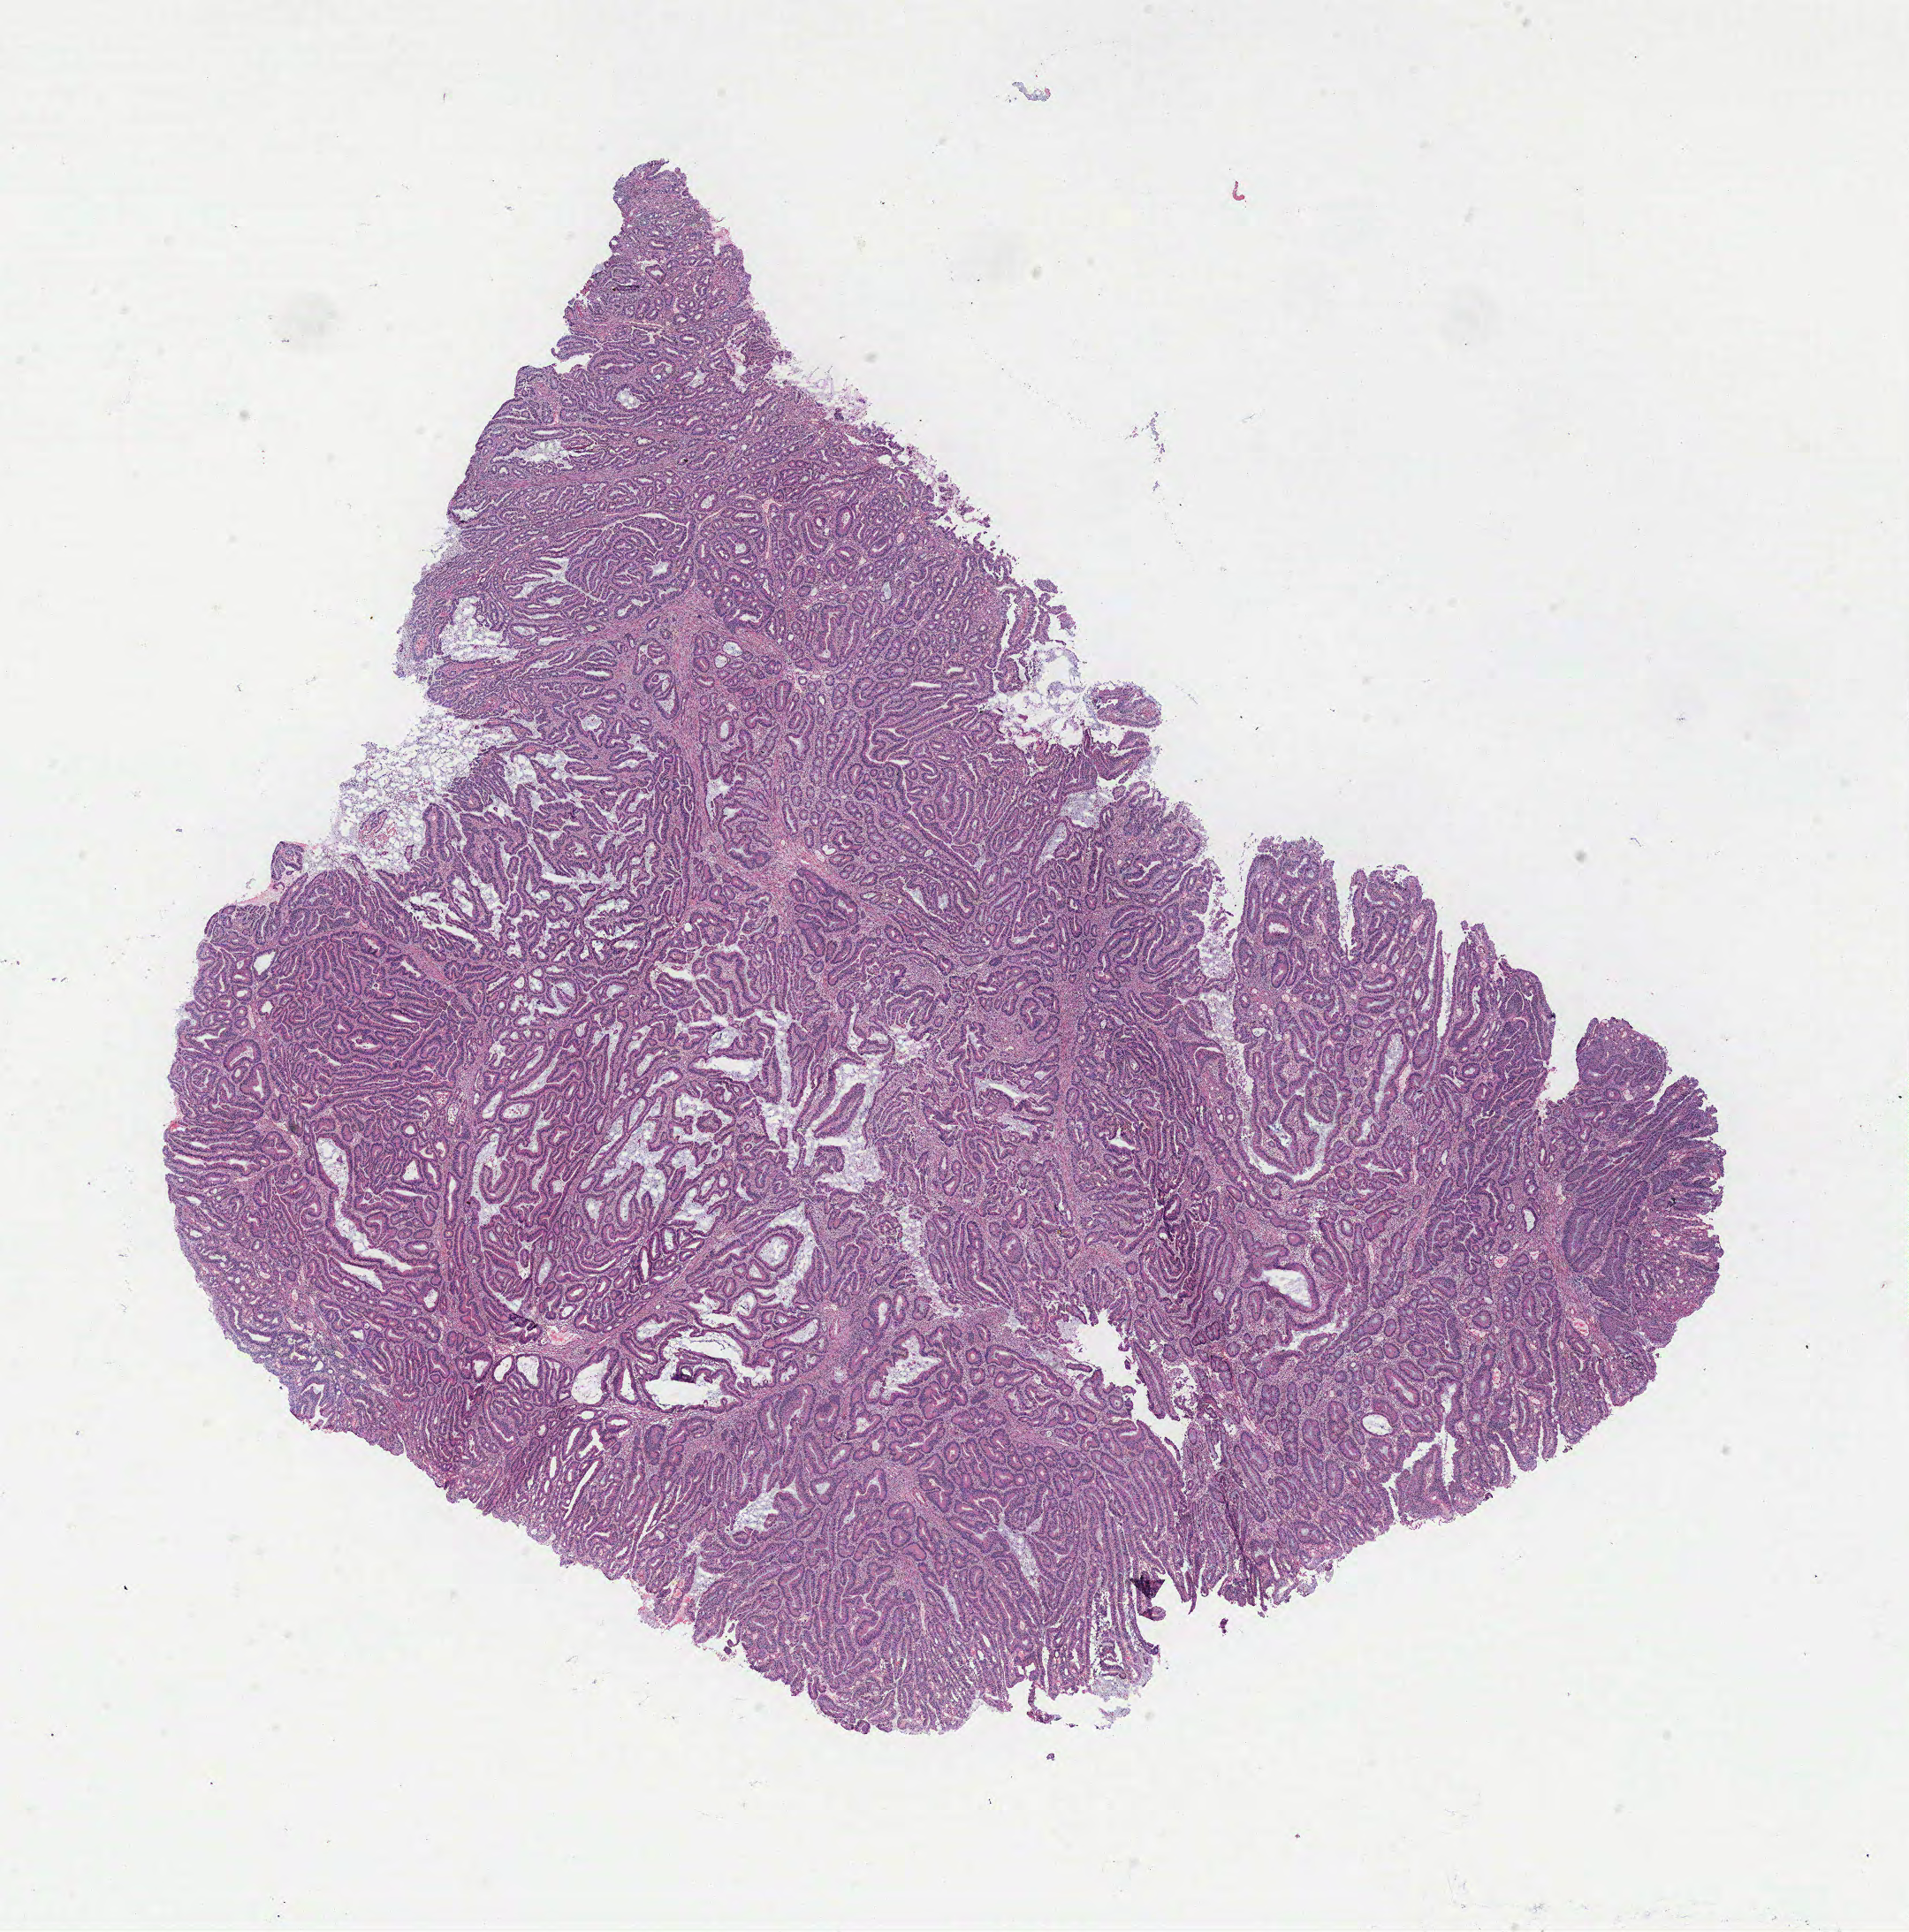
Whole-slide histology image, H&E — low-resolution overview of the scanned area, about 17.3 x 17.5 mm (acquisition: 40x scan). Tumour tissue sample, colon. 75-year-old female patient.
AJCC pathologic stage: I. Diagnosis: Adenocarcinoma, NOS. Primary tumour site (as recorded): colon.